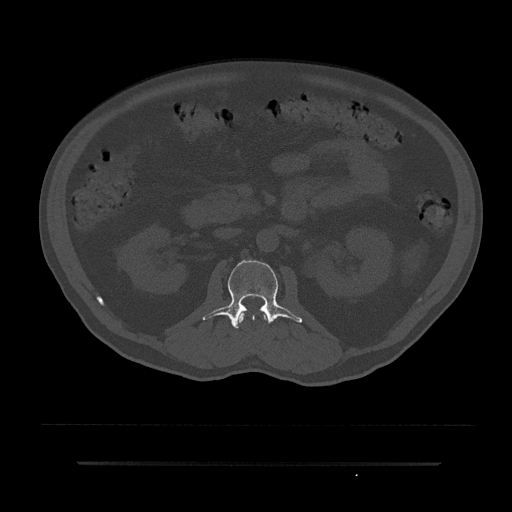
CT including the spine, one axial slice. Slice 86 of 797 in the series (ordered by position). Bone window (W 1800 / L 400 HU). 512 × 512 image matrix, field of view 464 × 464 mm. Patient: male, 59 years. Case-level facts recorded for this patient, not image findings: primary cancer: bile ducts; vertebrae with lytic lesions (as recorded): T10.
Outlined on this slice (semi-automatic segmentation, software-assisted and operator-edited):
- L1 vertebra: bounding box [x1, y1, x2, y2] px = [237, 311, 267, 325]
- L2 vertebra: [202, 260, 302, 328]